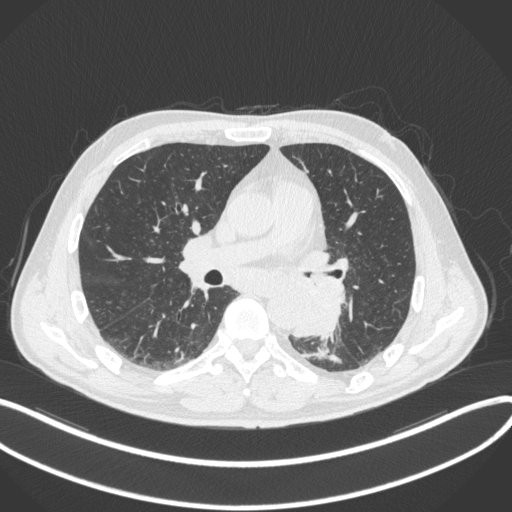
Chest CT, one axial slice. Slice 182 of 328 in the series (ordered by position). Reconstruction kernel B31f. 120 kVp. Lung window (W 1500 / L -600 HU). 512 × 512 image matrix, field of view 400 × 400 mm. Patient: male, 59 years. From the clinical record (not read from this slice): clinical TNM (as recorded): T2a N2 M0.
Structures marked on this image (bounding box drawn by a radiologist):
- lung tumour (recorded histology: squamous cell carcinoma): bounding box [x1, y1, x2, y2] px = [296, 275, 350, 339]